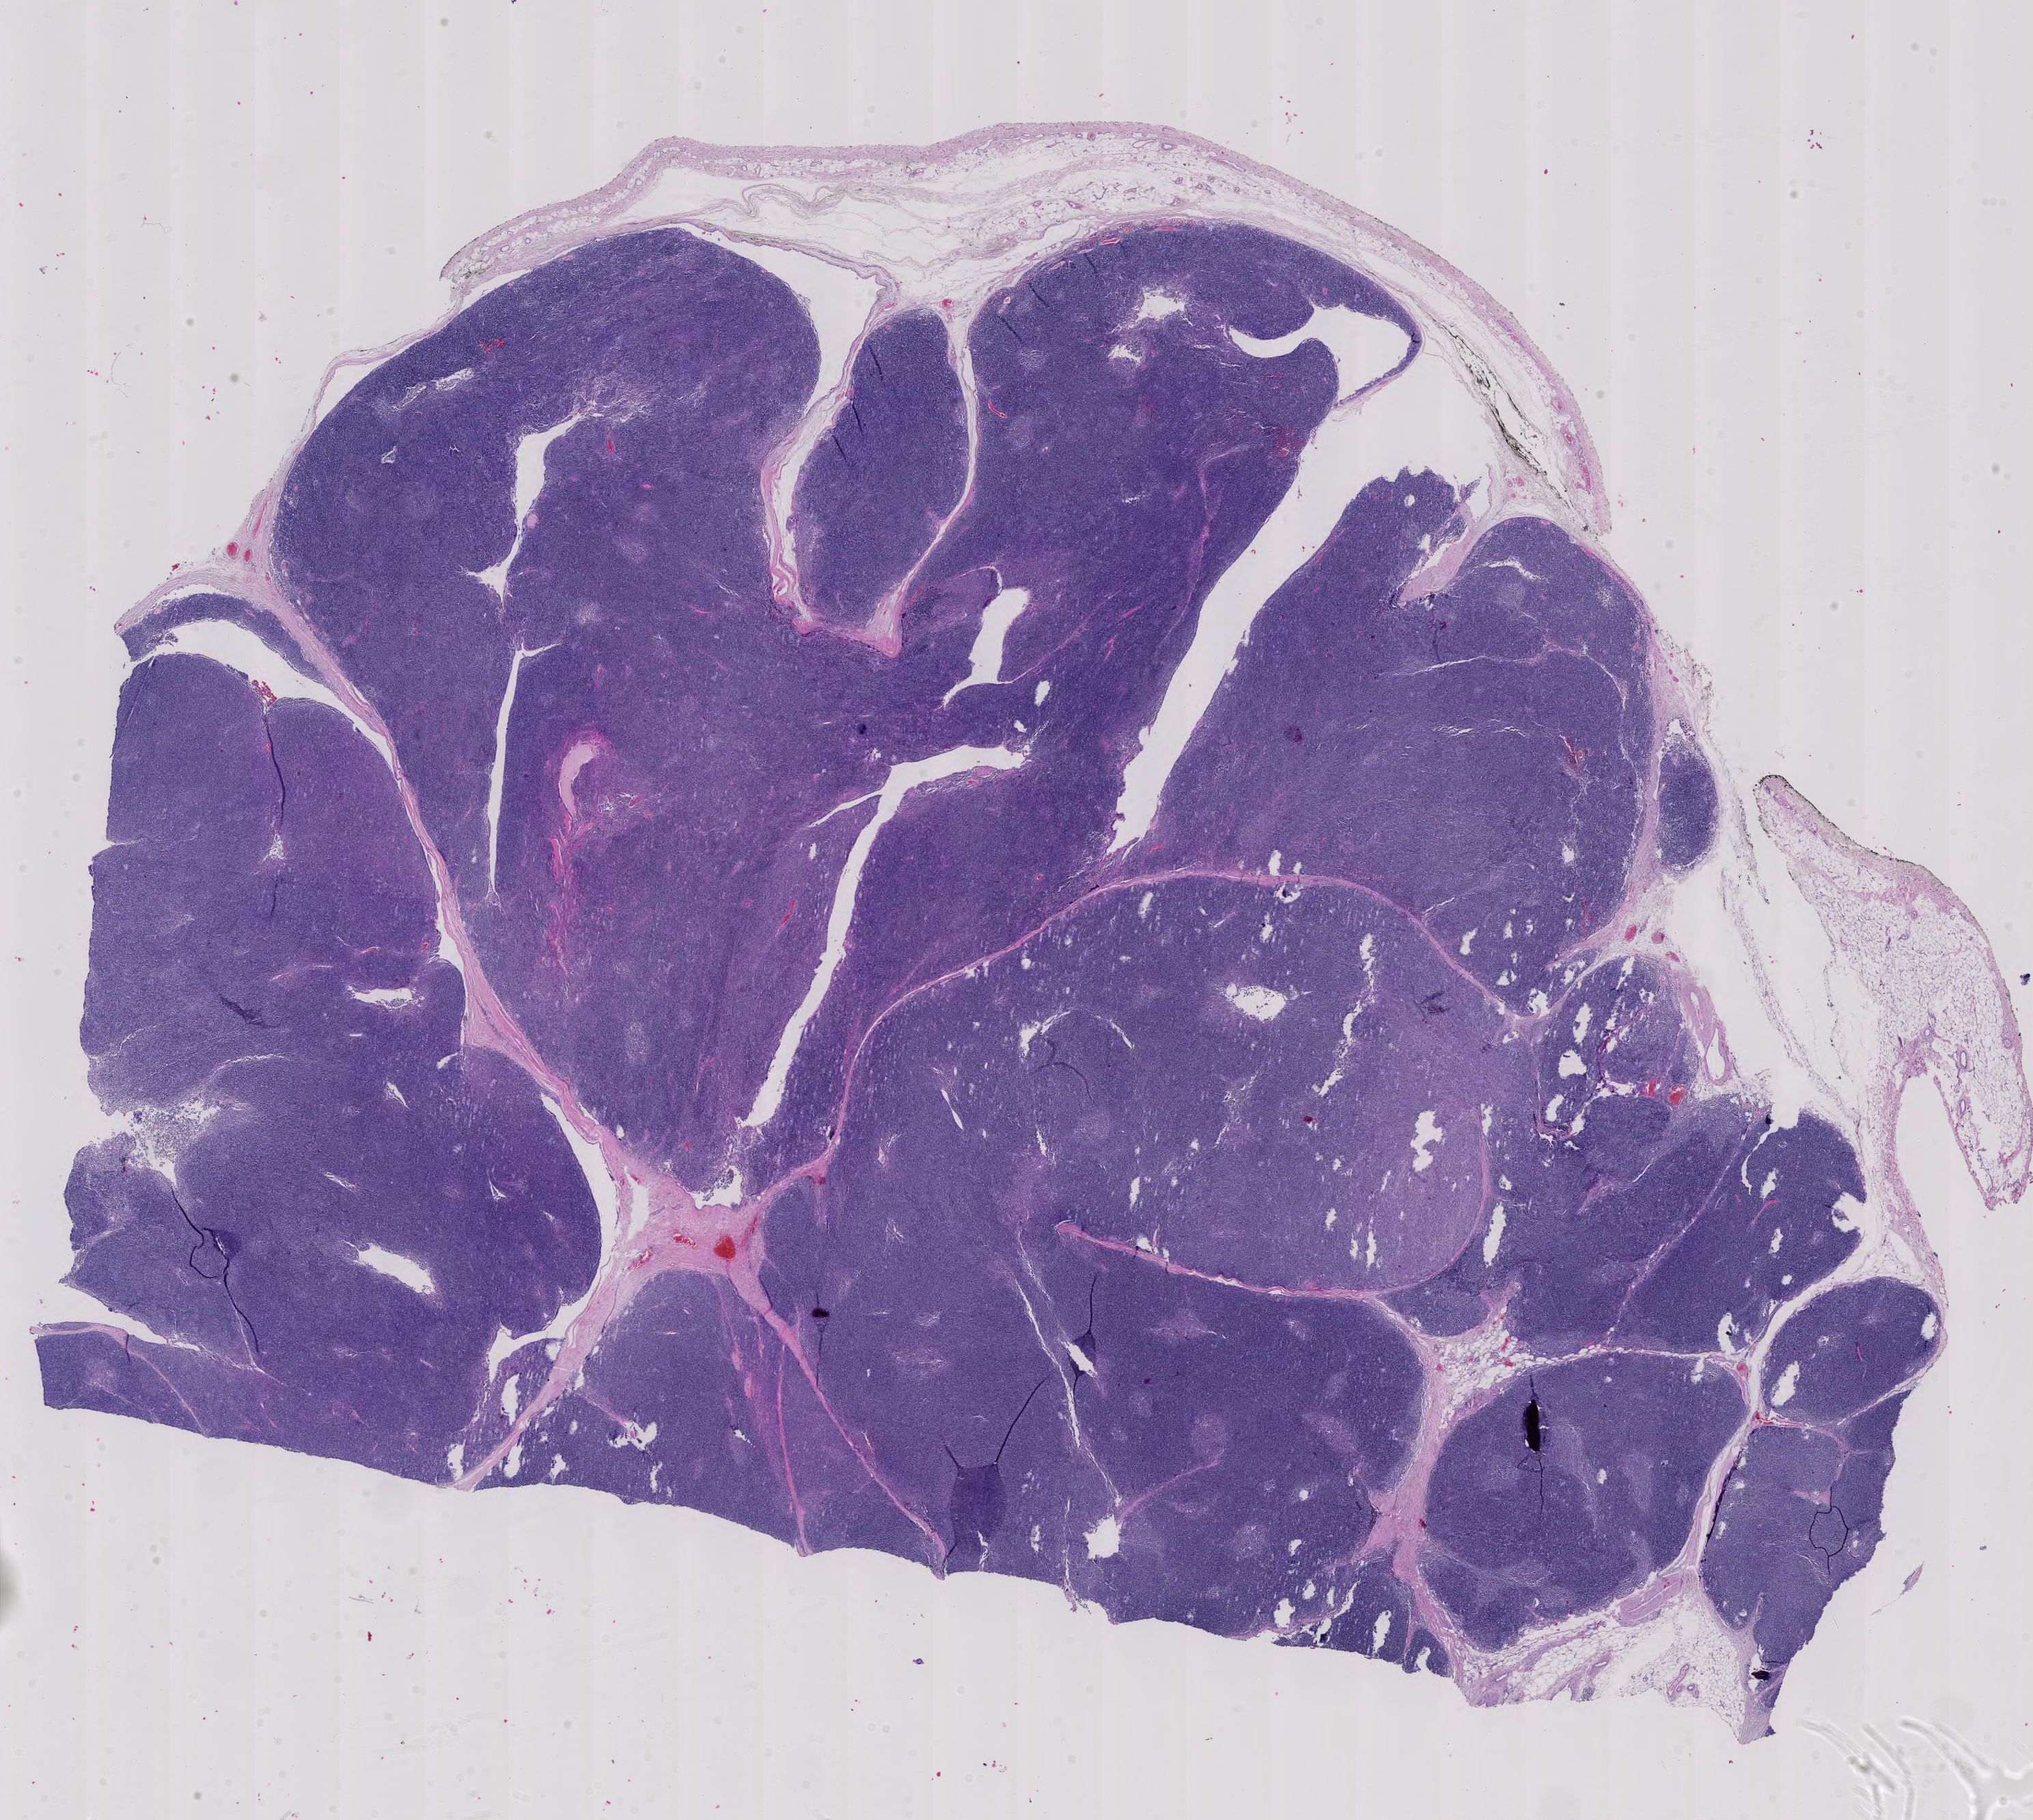
Whole-slide histology image, H&E-stained — low-resolution overview of the scanned area, about 21.7 x 19.4 mm; formalin-fixed paraffin-embedded (FFPE) diagnostic section; thymus, primary tumour sample. Male patient; age at initial diagnosis 59 years.
Pathologic diagnosis: Thymoma, type AB, malignant.